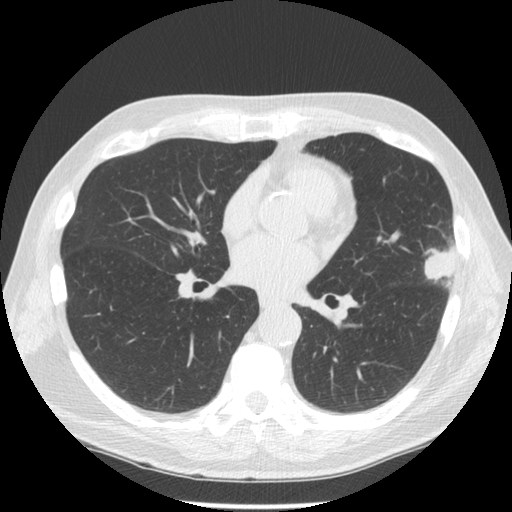
Low-dose screening chest CT, one axial slice; slice 69 of 134 in the series (ordered by position); reconstruction kernel STANDARD; 120 kVp; lung window (W 1500 / L -600 HU); 2.5 mm slice thickness; 512 × 512 image matrix, field of view 350 × 350 mm.
Structures marked on this image (expert manual segmentation):
- lesion 1 (tumor, upper lobe of left lung): bounding box [x1, y1, x2, y2] px = [424, 249, 457, 281]